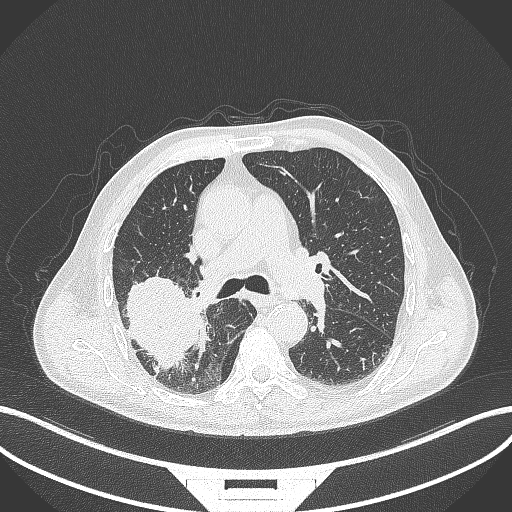
Chest CT, one axial slice; slice 254 of 429 in the series (ordered by position); reconstruction kernel B70f; 120 kVp; lung window (W 1500 / L -600 HU); 512 × 512 image matrix, field of view 400 × 400 mm. Male patient, age 72 years. Case-level facts recorded for this patient, not image findings: clinical TNM (as recorded): T3 N2 M0.
Outlined on this slice (bounding box drawn by a radiologist):
- lung tumour (recorded histology: adenocarcinoma): box from (x=115, y=276) to (x=207, y=374) px